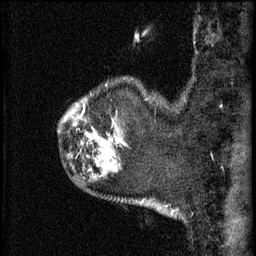
Breast MRI (dynamic contrast-enhanced), one sagittal slice. Slice 52 of 60 in the series (ordered by position). 3 images stored at this slice position (order not interpretable as contrast timing). 1.5 T. TE 4.2 ms, TR 11 ms. 256 × 256 image matrix, field of view 180 × 180 mm. Female patient, age 52 years.
Annotated regions visible in this slice (semi-automatic segmentation, software-assisted and operator-edited):
- analysis volume of interest (the breast-tissue region the enhancement analysis was run in; not a lesion): bounding box [x1, y1, x2, y2] px = [86, 94, 129, 157]
- tumour enhancement mask (voxels above the 70 % enhancement threshold inside the analysis volume of interest): [86, 134, 102, 143]